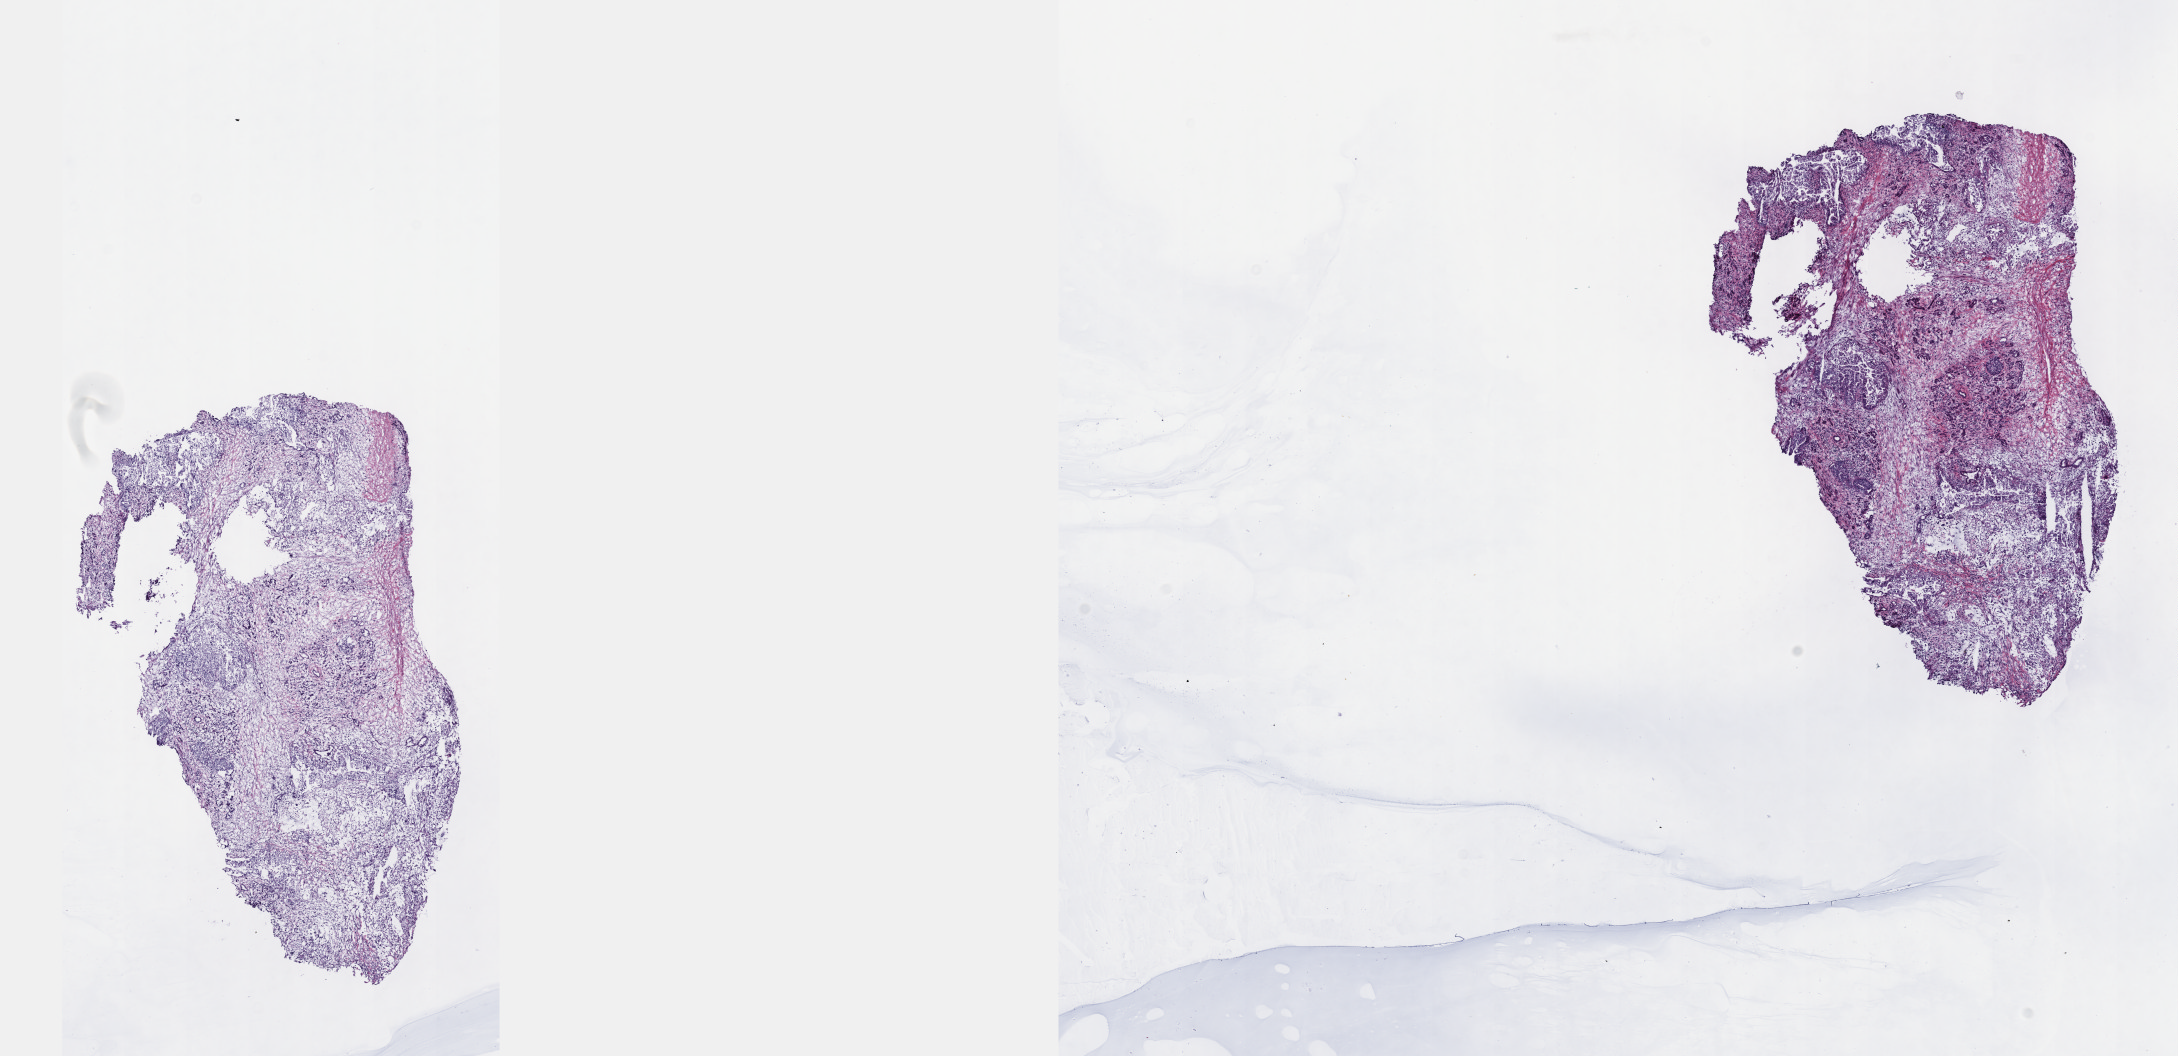
Whole-slide histology image, Hematoxylin and eosin (H&E) stained — shown as a low-resolution overview of the whole scanned area (about 17.6 x 8.5 mm, from a 40x scan), frozen section, pancreas, primary tumour sample. Male patient; age at initial diagnosis 50 years. Histologic grade: G3 (poorly differentiated). Composition of this section per pathologist review: tumour cells 25%, tumour nuclei 55%, normal cells 15%, stromal cells 58%, necrosis 2%. Inflammatory infiltration, as recorded: lymphocyte infiltration 12%, monocyte infiltration 5%, neutrophil infiltration 2%.
Histologic diagnosis: Infiltrating duct carcinoma, NOS (head of pancreas). AJCC pathologic stage: IIB (7th edition).